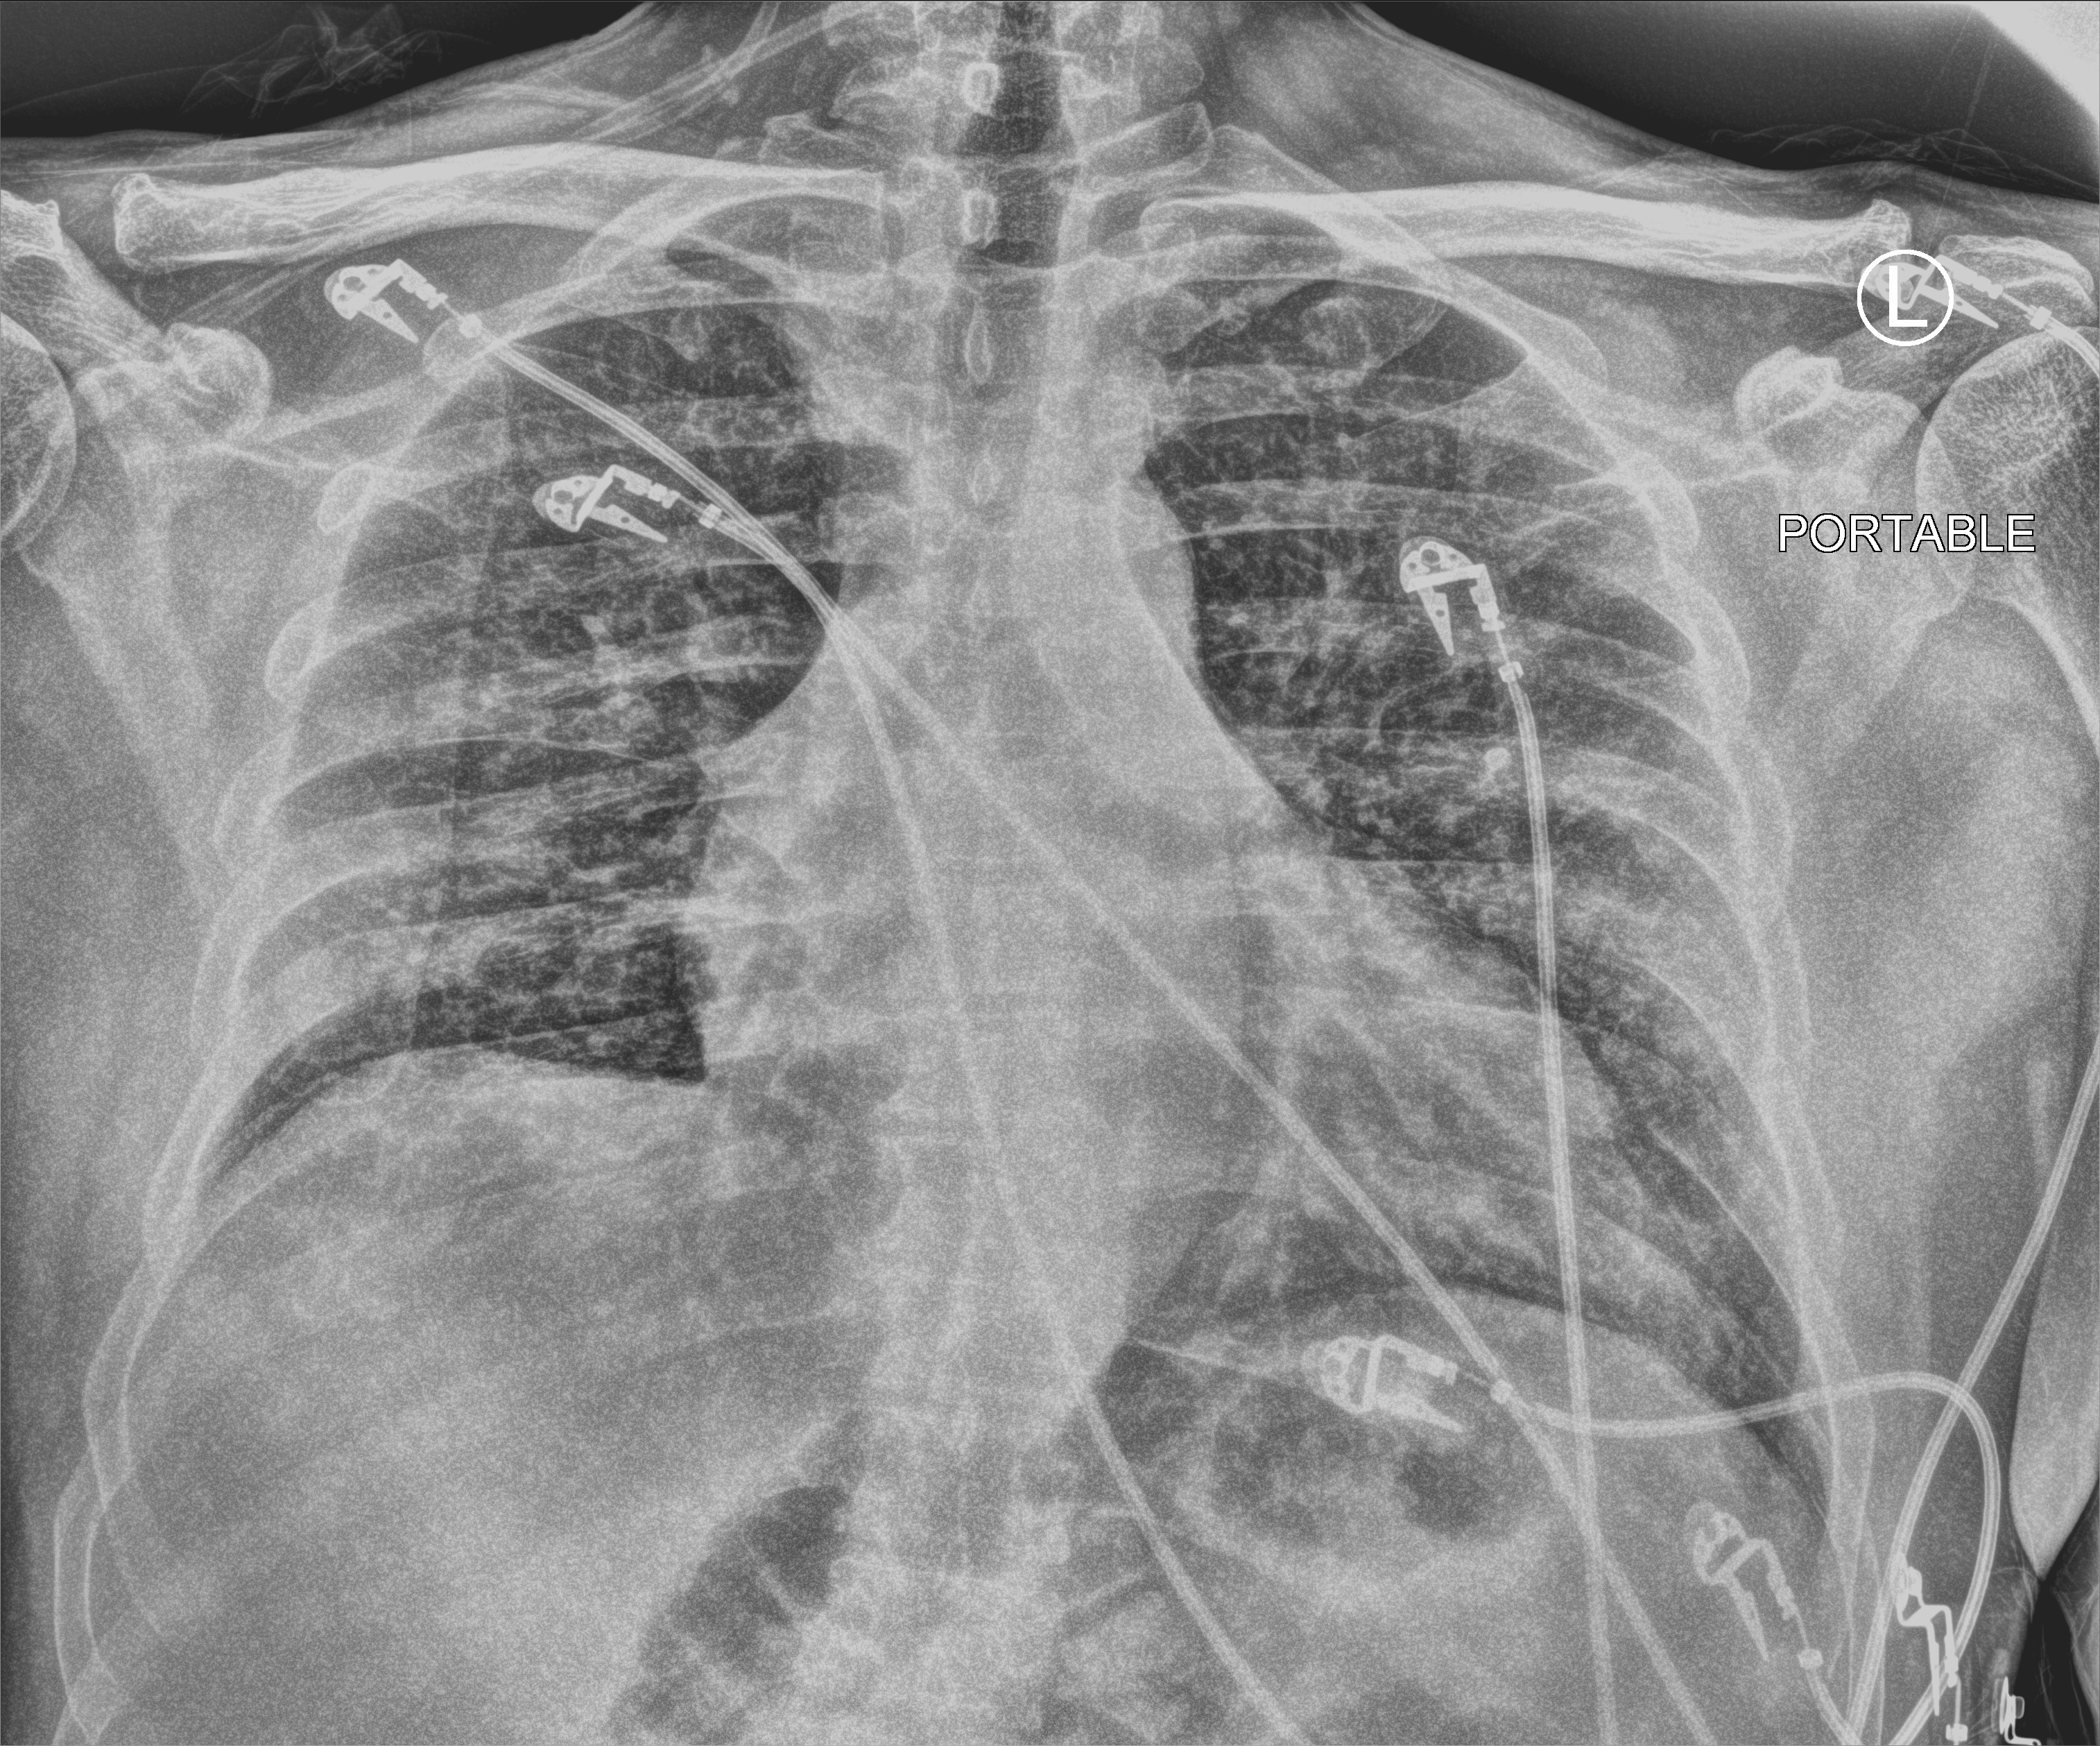
Bedside chest radiograph (computed radiography); anteroposterior (AP) projection. Patient hospitalised with COVID-19; male, aged 18–59 years.
Admission-level facts for this patient (not findings on this image; timing relative to this image not recorded): admitted to intensive care during this hospital stay: no; hypertension (admission record): no; mechanically ventilated during this hospital stay: no.